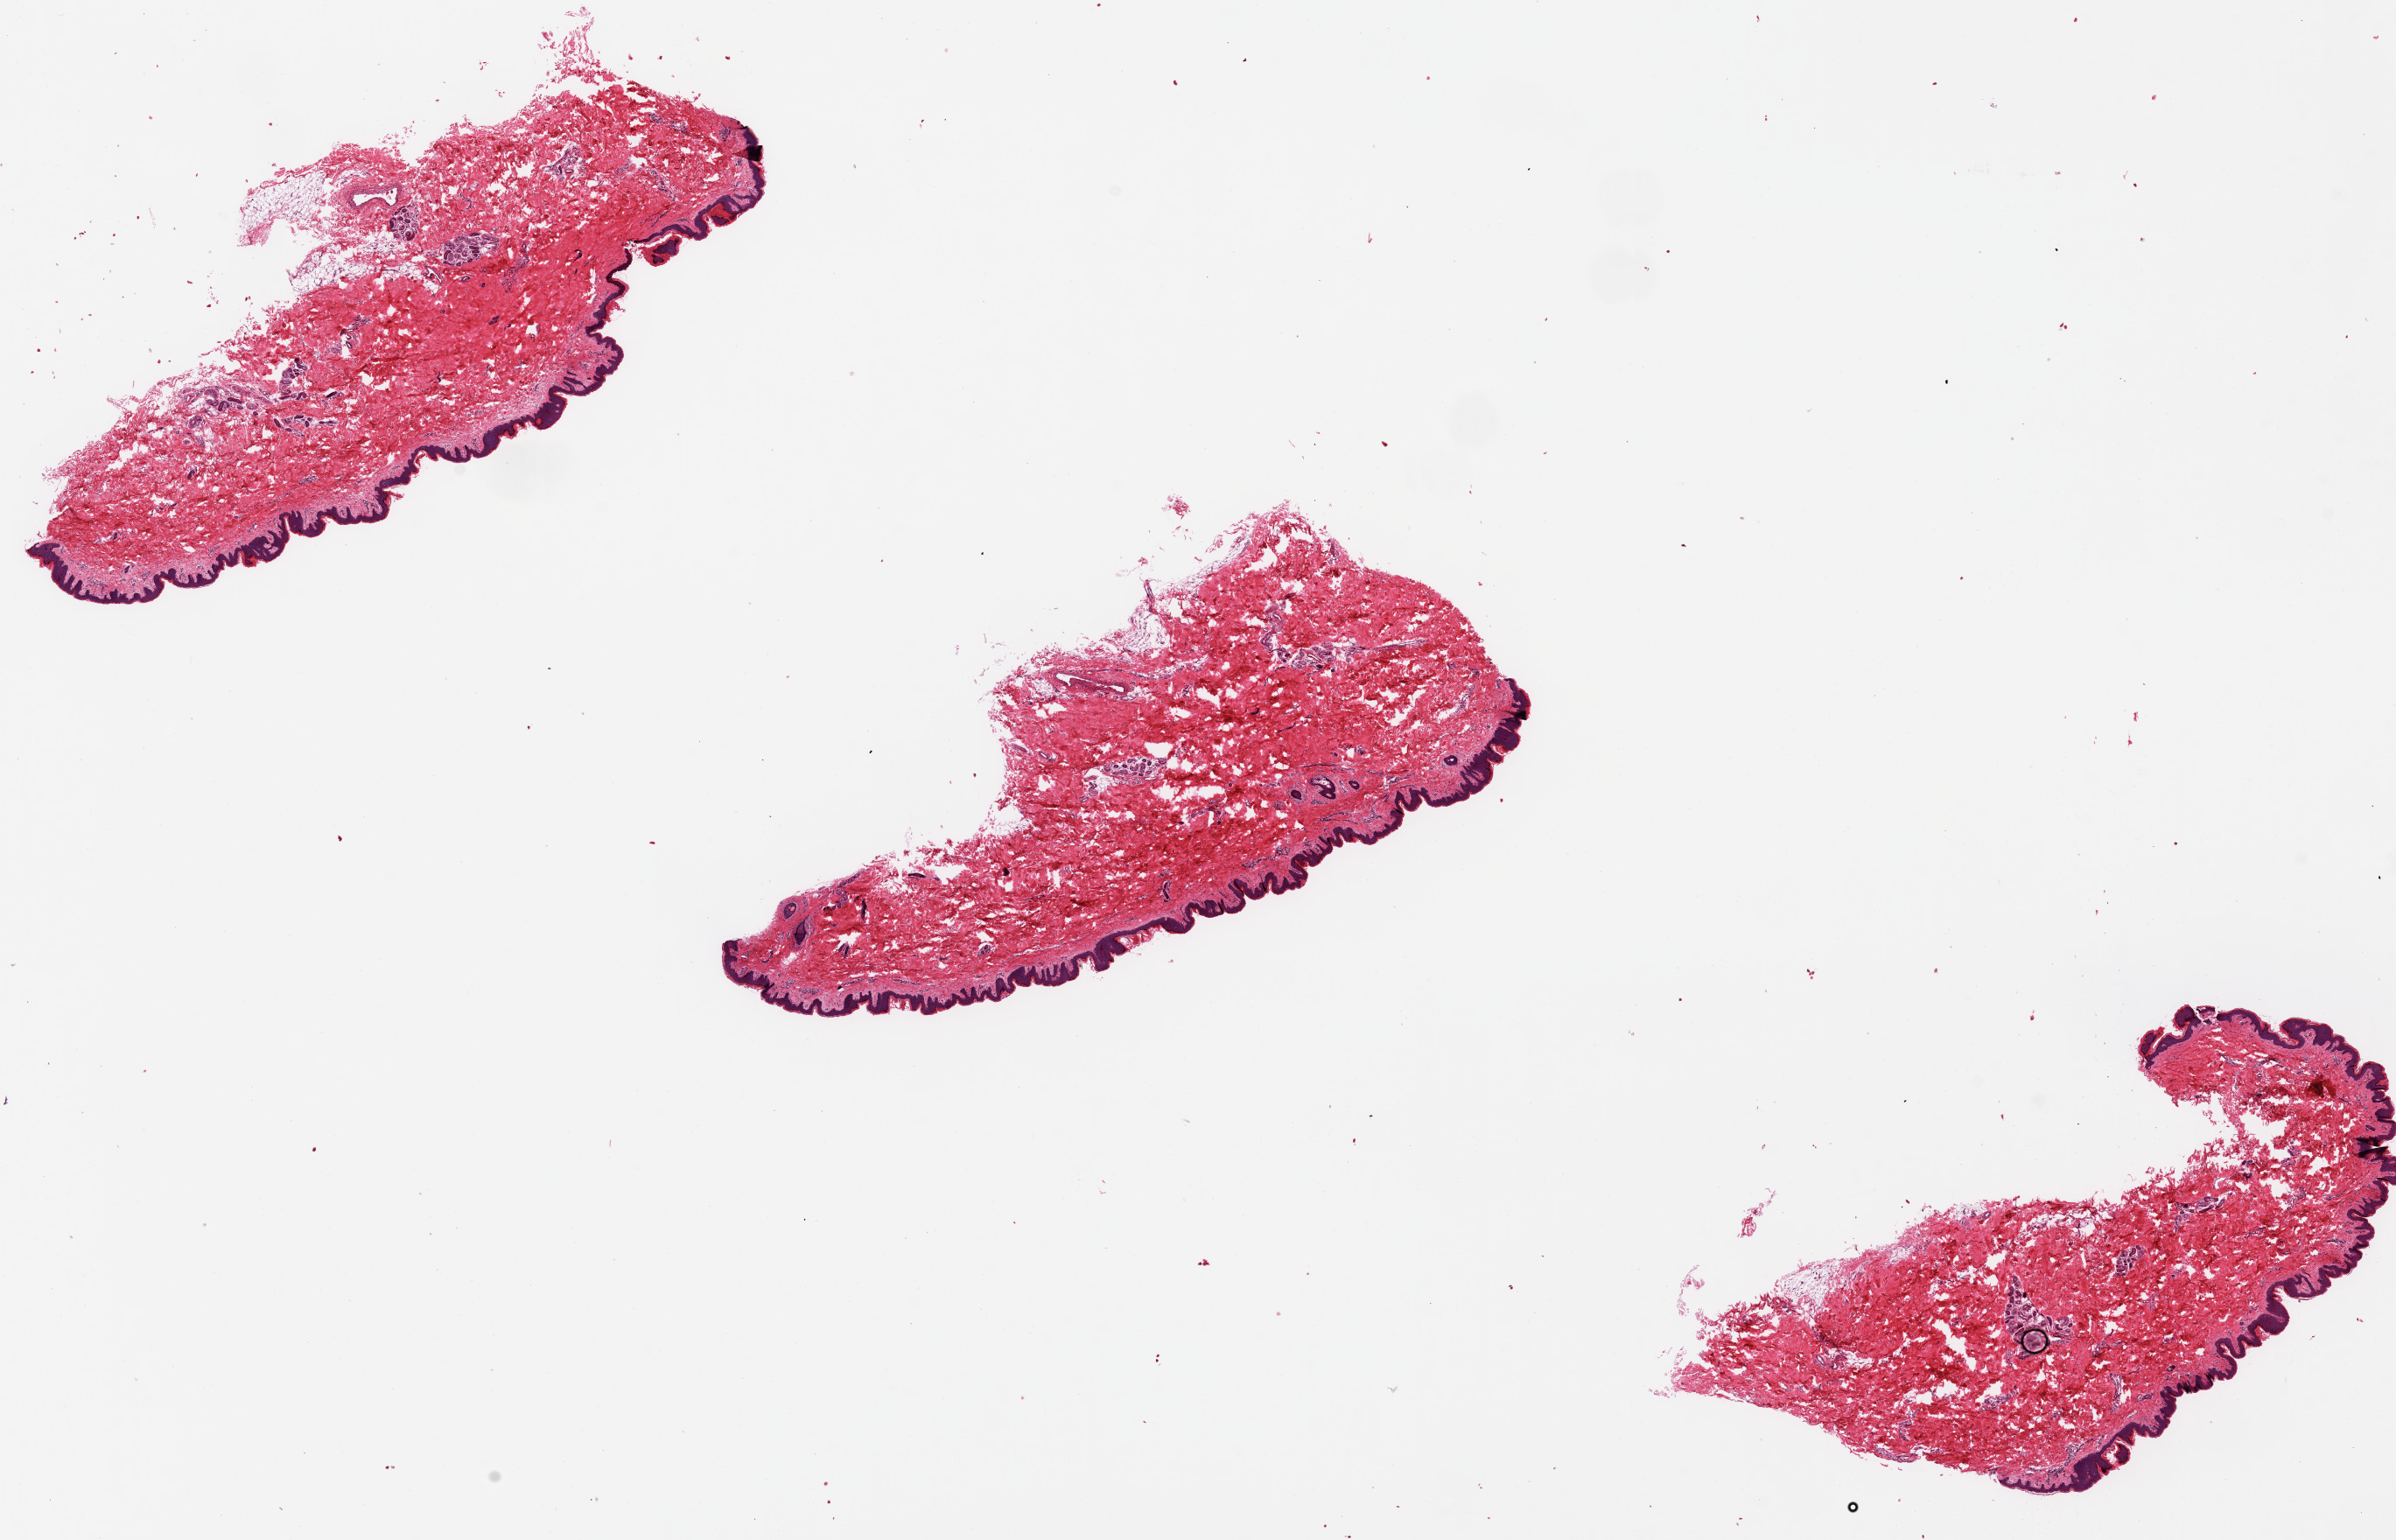
Digitized haematoxylin and eosin-stained section, a low-resolution overview of the entire scanned area, about 21.7 x 13.9 mm (from a 20x scan); PAXgene-fixed, paraffin-embedded tissue; target tissue: skin of lower leg; donor tissue sample. Donor sex: male.
Review note (as recorded): 3 pieces; no lesions.